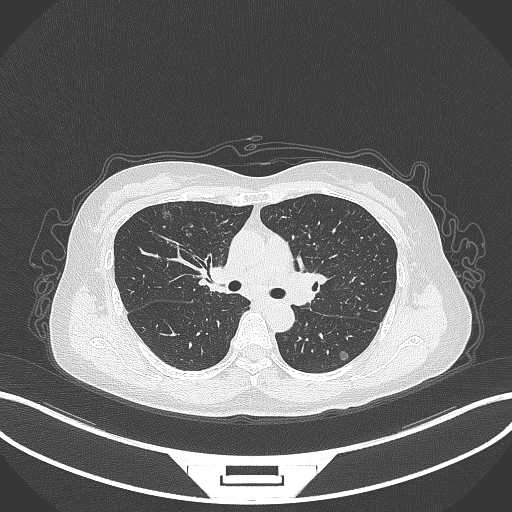
Chest CT, one axial slice; slice 203 of 315 in the series (ordered by position); 120 kVp; lung window (W 1500 / L -600 HU); 512 × 512 image matrix, field of view 400 × 400 mm. Patient: female, 61 years. From the clinical record (not read from this slice): clinical TNM (as recorded): T1b N0 M0; histopathological grade: G1.
Outlined on this slice (bounding box drawn by a radiologist):
- lung tumour (recorded histology: adenocarcinoma): bounding box [x1, y1, x2, y2] px = [160, 208, 172, 221]